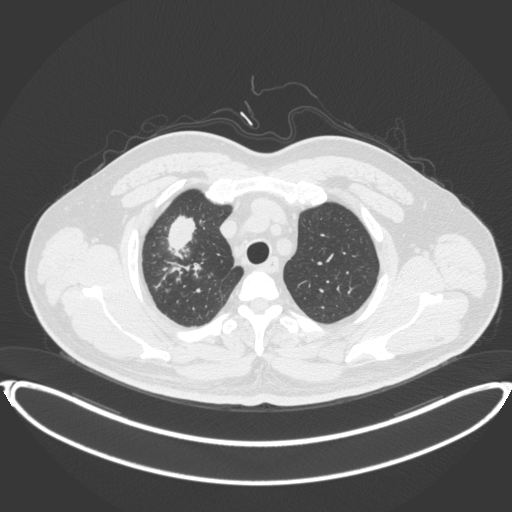
Chest CT, one axial slice. Position 320 of 399 along the scan axis. Reconstruction kernel B31f. 120 kVp. Lung window (W 1500 / L -600 HU). 1 mm slice thickness. 512 × 512 image matrix, field of view 445 × 445 mm. Male patient, age 53 years. Case-level facts recorded for this patient, not image findings: clinical TNM (as recorded): T2a N0 M0.
Annotated regions visible in this slice (rectangle marked by the reading radiologist):
- lung tumour (recorded histology: adenocarcinoma): bounding box (x1, y1, x2, y2) in pixels: (162, 211, 198, 258)